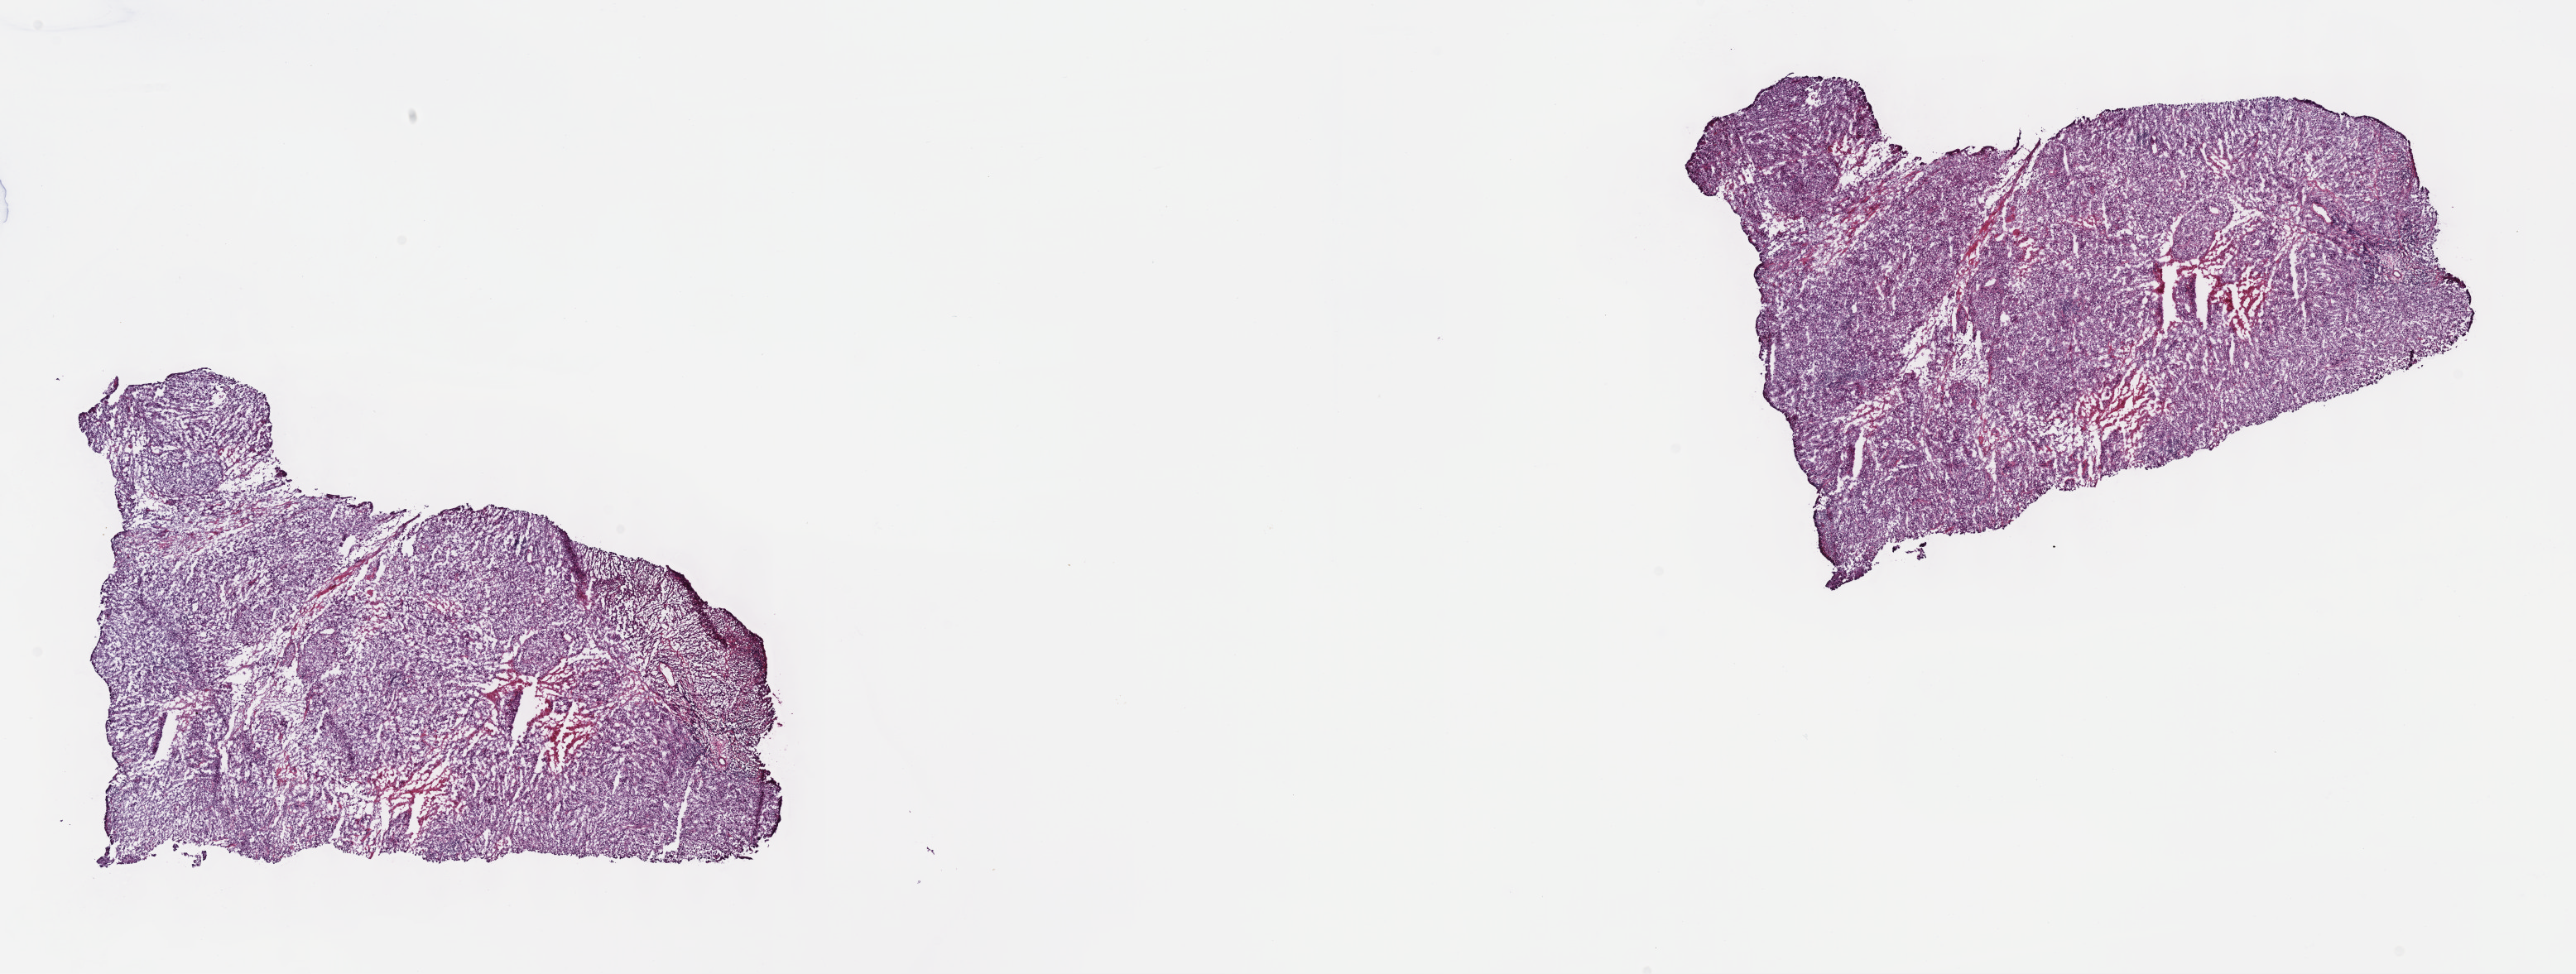
Digitized H&E tissue section (whole slide), low-resolution overview of the scanned area, about 25.2 x 9.5 mm (from a 40x scan), frozen section from the top of the tissue portion, metastatic tumour sample, sampled site: lymph nodes of head, face and neck. Patient: male, age at initial diagnosis 73 years. Slide review estimates, as recorded: tumour cells 95%, tumour nuclei 95%.
This section: metastatic tumour tissue. Patient diagnosis: Malignant melanoma, NOS.